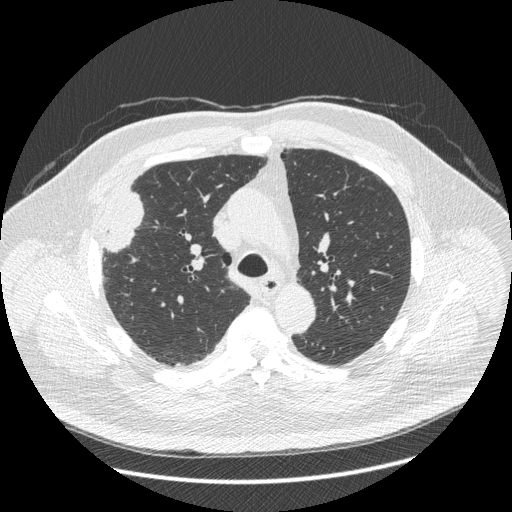
Low-dose screening chest CT, one axial slice. Position 294 of 426 along the scan axis. Lung window (W 1500 / L -600 HU). 1.25 mm slice thickness. 512 × 512 image matrix, field of view 400 × 400 mm.
Outlined on this slice (outlined manually by an expert reader):
- lesion 1 (tumor, upper lobe of right lung): bounding box (x1, y1, x2, y2) in pixels: (106, 192, 144, 252)